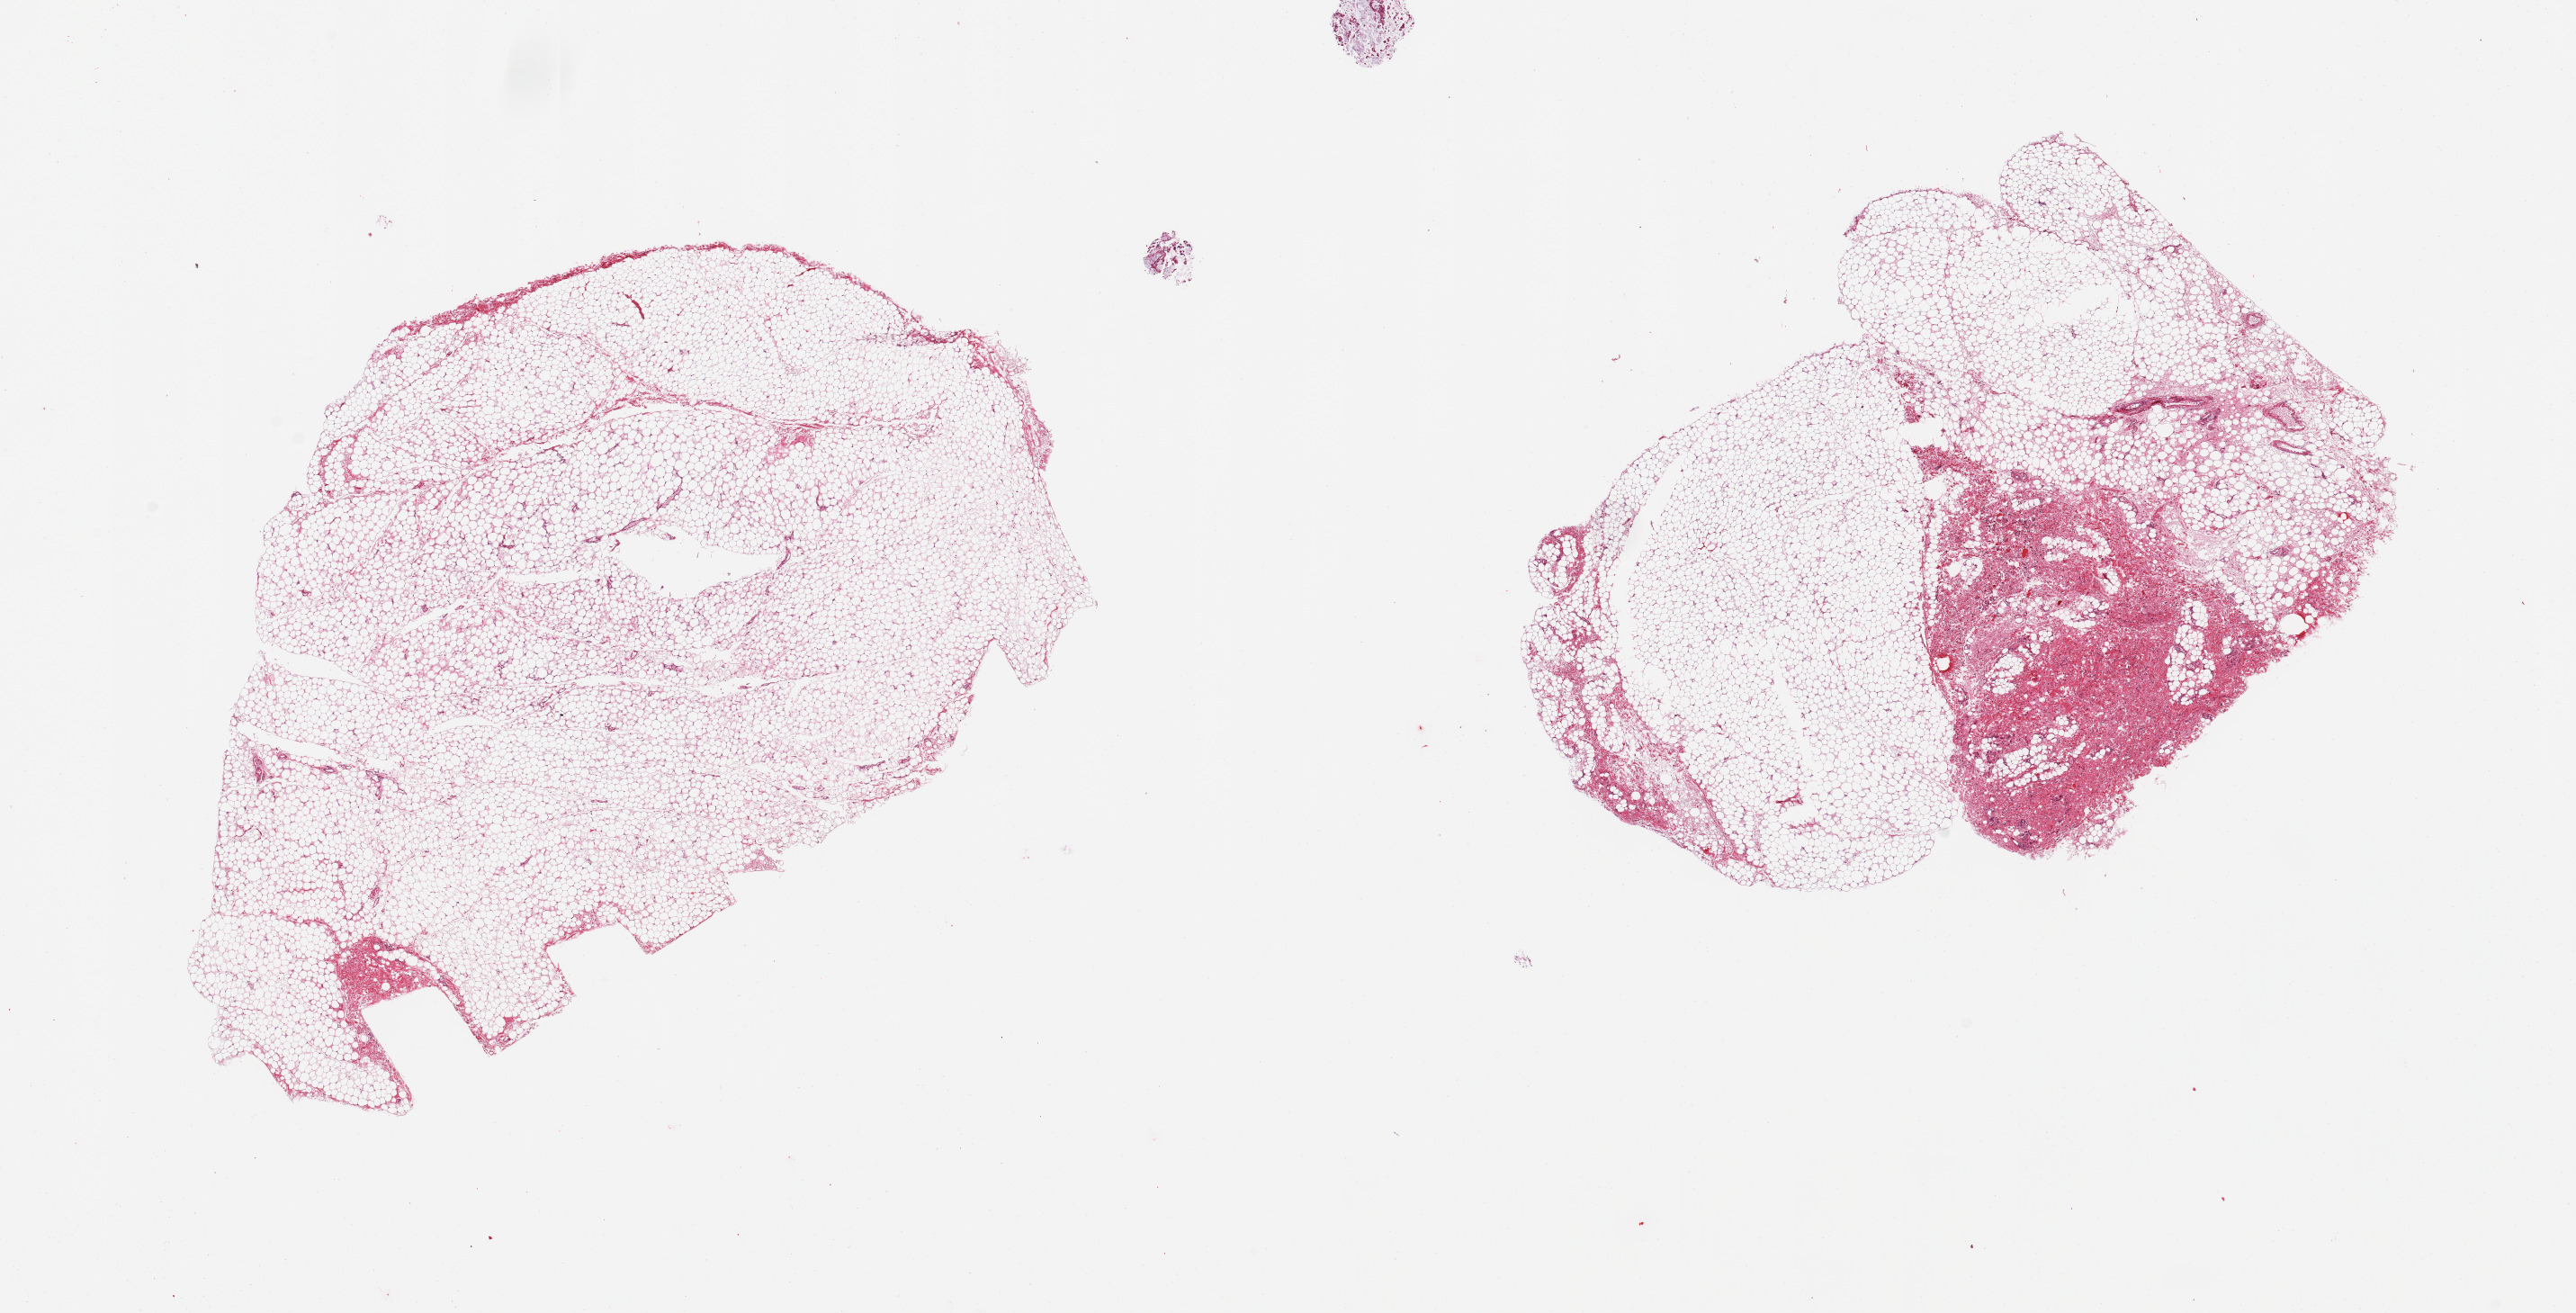
H&E whole-slide image, brightfield — whole scanned area (about 22.6 x 11.5 mm, from a 20x scan) shown as a low-resolution overview, PAXgene-fixed paraffin-embedded (PFPE) section, target tissue: thyroid, donor tissue sample. Male donor.
Pathologist's review note for this sample: 2 pieces; fat only.